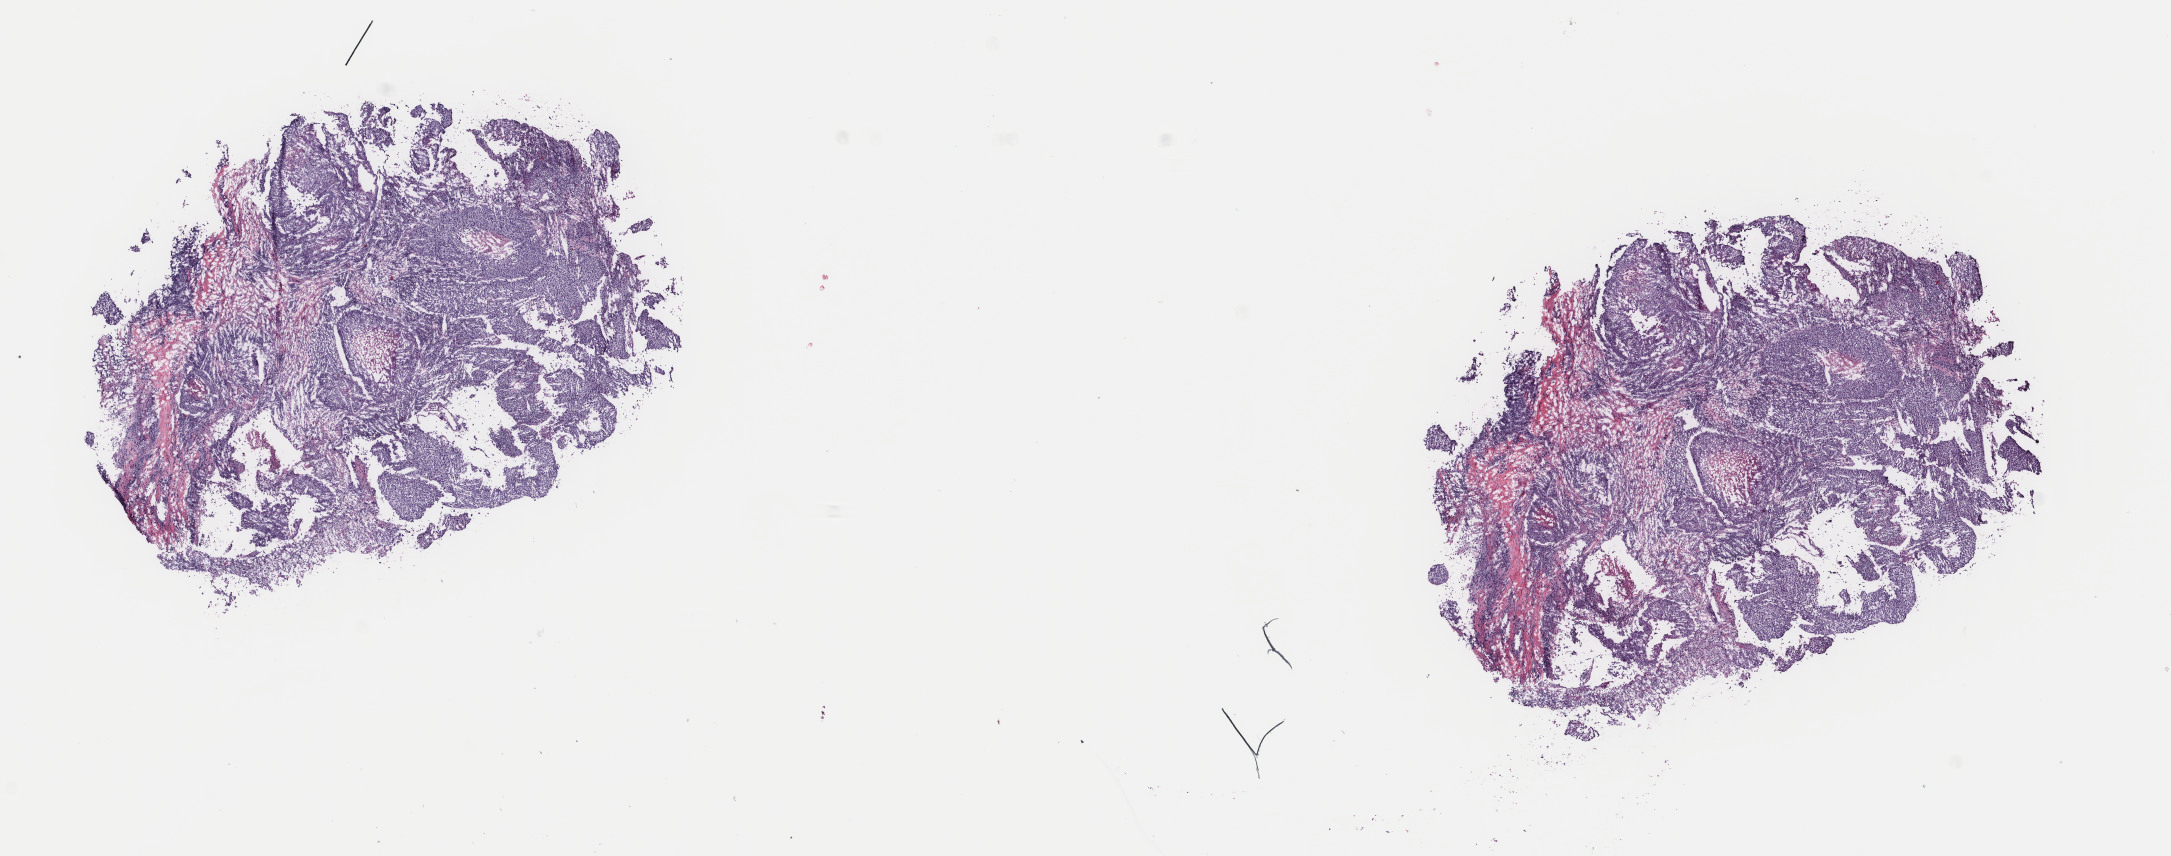
Whole-slide histology image, H&E, a low-resolution overview of the entire scanned area, about 17.2 x 6.8 mm (from a 40x scan). Frozen section from the top of the tissue portion. Head and neck, primary tumour sample. Male, age 50 years at initial diagnosis. Histologic grade: G3 (poorly differentiated). Slide review estimates, as recorded: tumour cells 85%, tumour nuclei 85%, normal cells 0%, stromal cells 10%, necrosis 5%. Infiltration values recorded for this section: lymphocyte infiltration 40%, monocyte infiltration 20%, neutrophil infiltration 20%.
- AJCC pathologic stage: IVB (6th edition)
- pathologic diagnosis: Squamous cell carcinoma, NOS (tonsil, NOS)